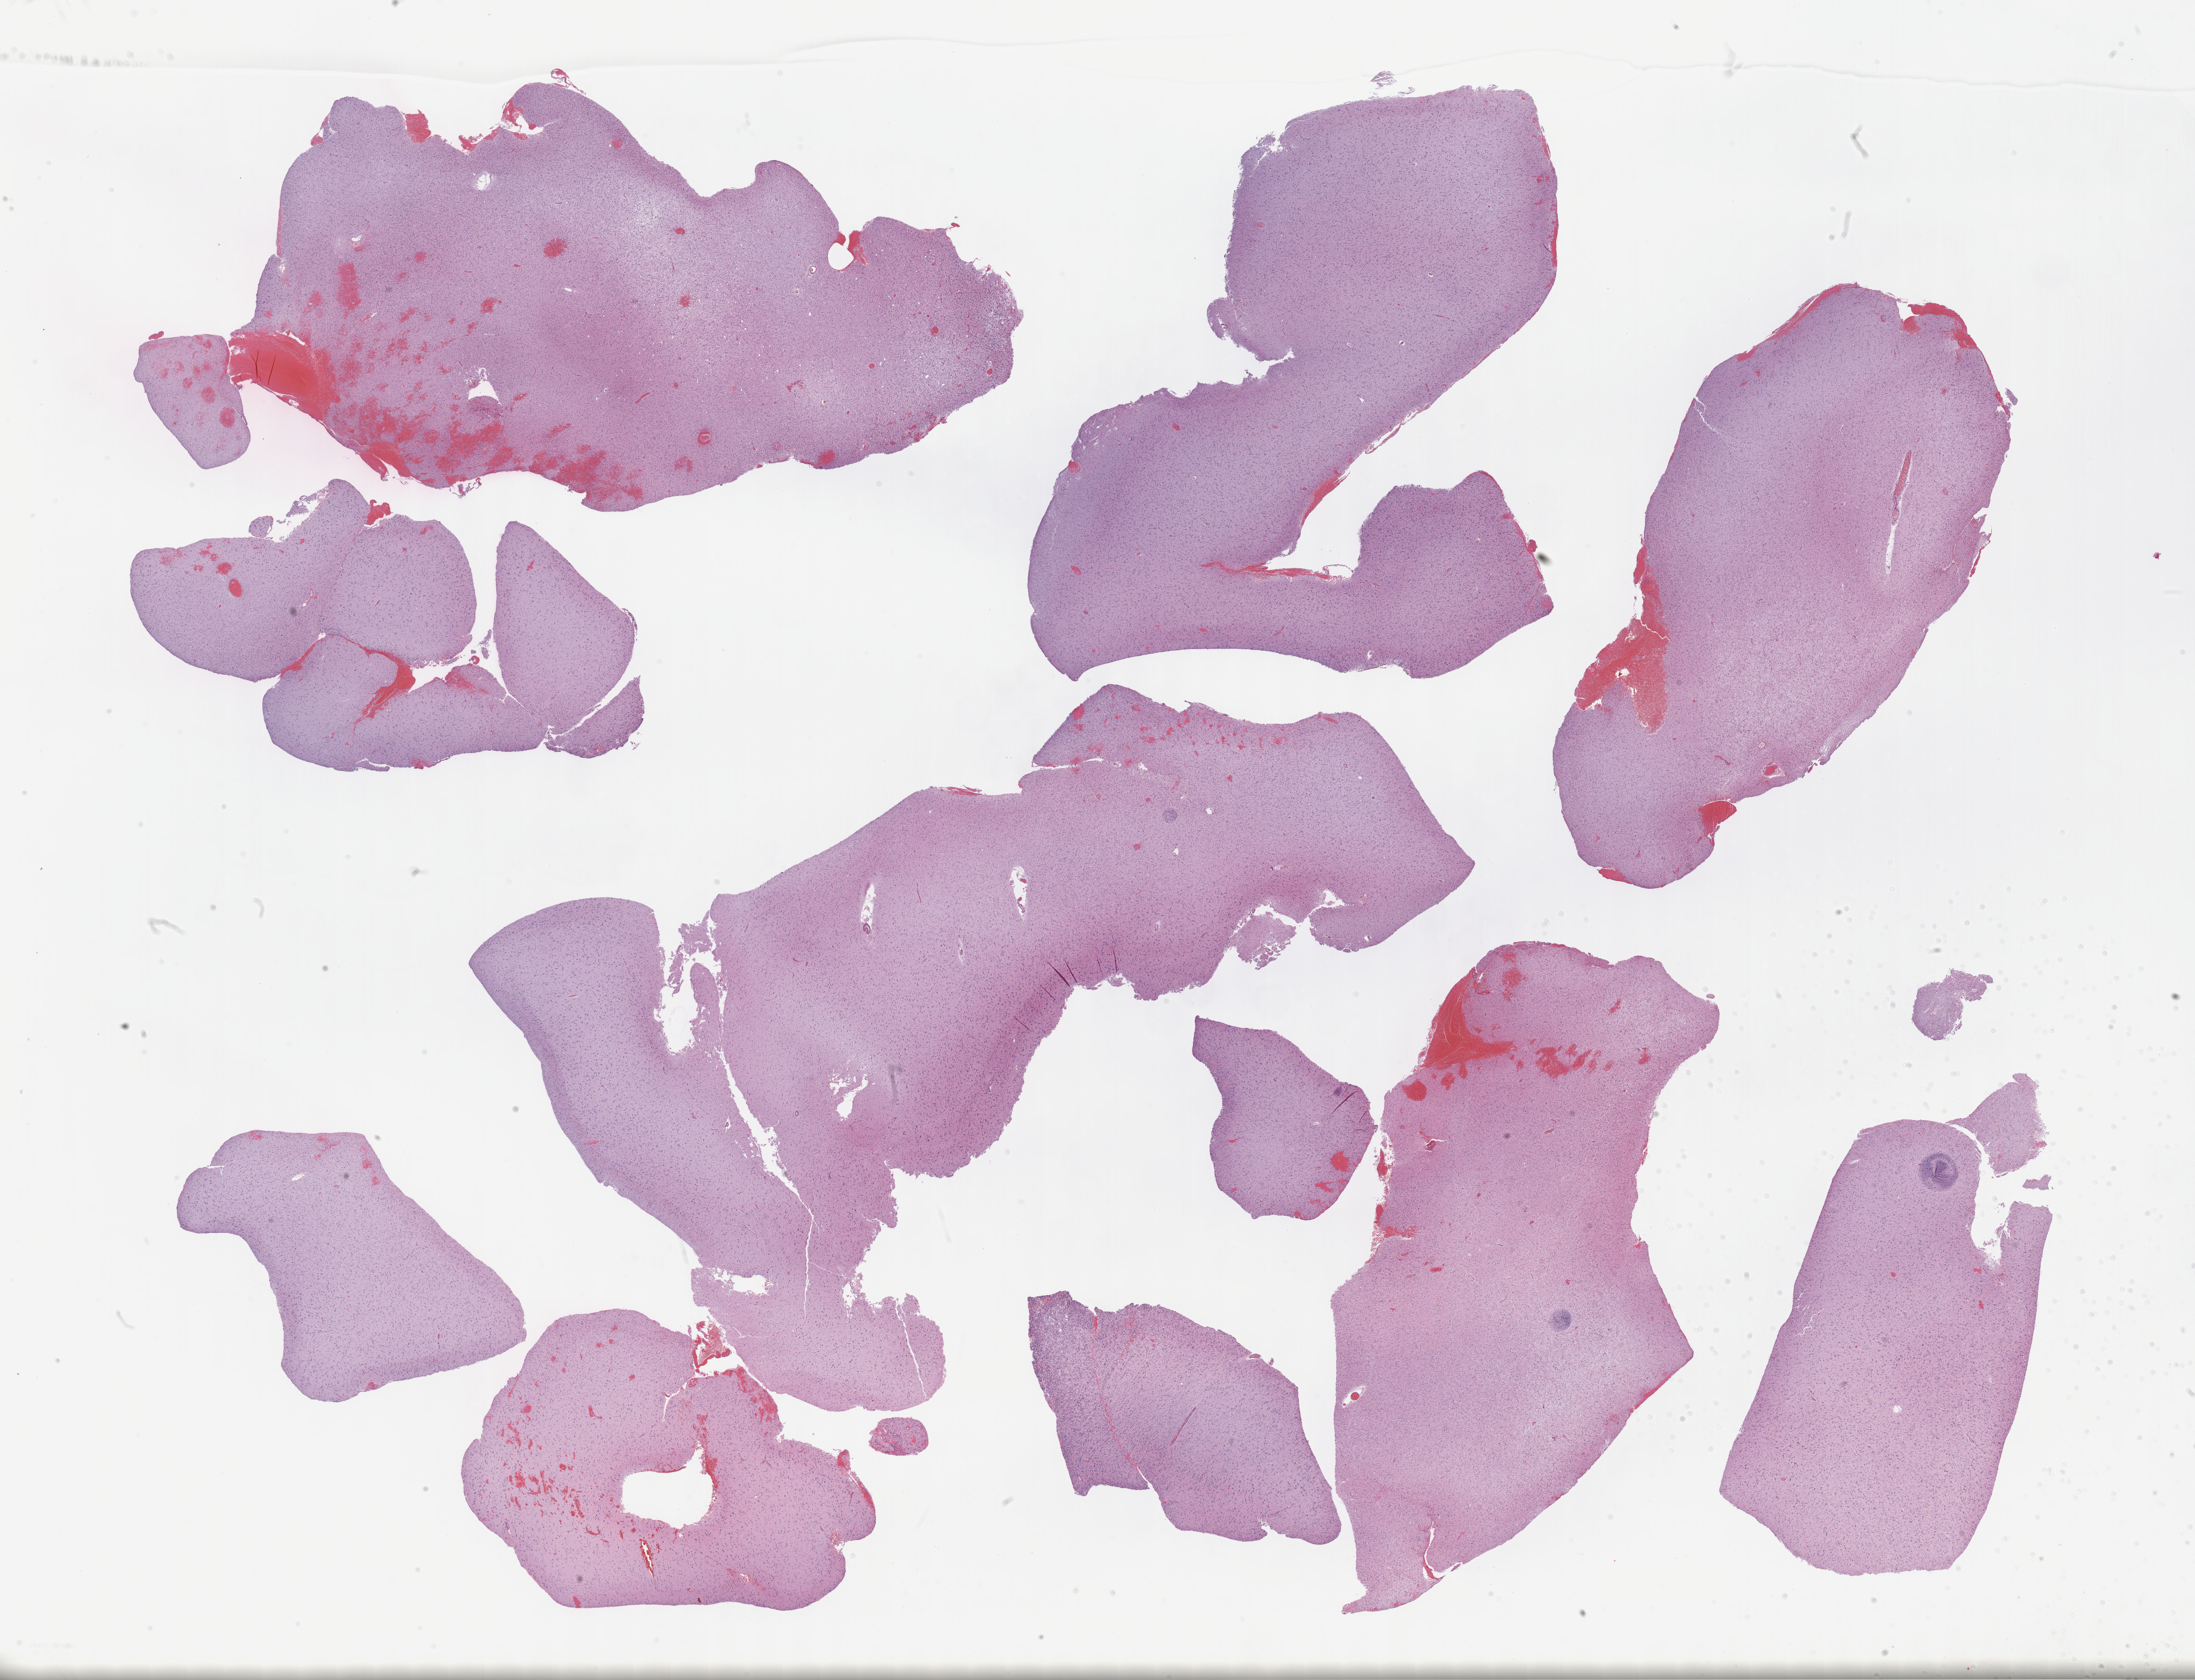
Whole-slide histology image, H&E — low-resolution overview of the scanned area, about 29.7 x 22.7 mm (acquisition: 40x scan), formalin-fixed paraffin-embedded (FFPE) diagnostic section, brain, primary tumour sample. Patient: male, age at initial diagnosis 54 years. Histologic grade: G2 (moderately differentiated).
Histologic diagnosis: Oligodendroglioma, NOS (cerebrum). Laterality: left.